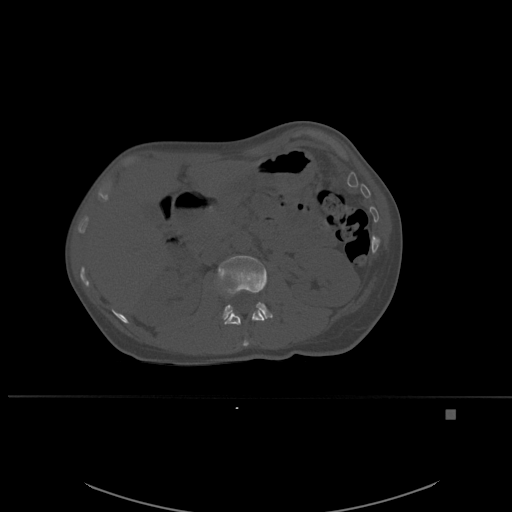
CT including the spine, one axial slice. Slice 247 of 537 in the series (ordered by position). Bone window (W 1800 / L 400 HU). 1.5 mm slice thickness. 512 × 512 image matrix. Female patient, age 45 years. From the clinical record (not read from this slice): primary cancer: lung.
Annotated regions visible in this slice (semi-automatically segmented with operator editing):
- L1 vertebra: bounding box [x1, y1, x2, y2] px = [224, 309, 266, 347]
- L2 vertebra: [218, 256, 273, 320]